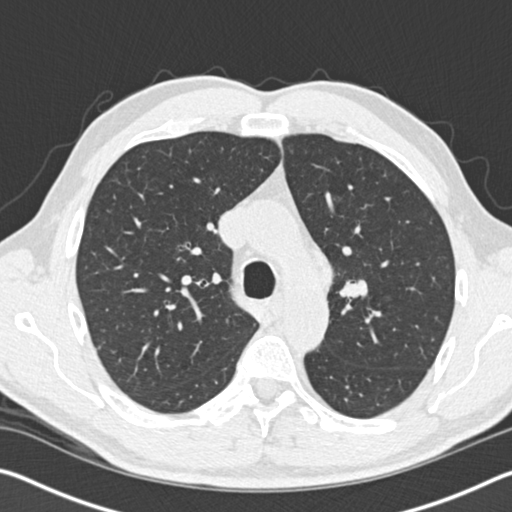
Low-dose screening chest CT, axial slice, baseline screening round, lung window (W 1500 / L -600 HU), 2 mm slice thickness, standard (soft-tissue) reconstruction kernel (B30f), 512 × 512 image matrix. Male, age 61 years at enrolment. Former smoker at enrolment.
Lesion marked by an expert reader, bounding box (x1, y1, x2, y2) in pixels: (343, 274, 373, 314). The screening reader recorded 2 non-calcified nodules or masses ≥4 mm on this exam; which of them this box marks is not recorded. Official screen result: positive, change unspecified: nodule(s) >= 4 mm or enlarging nodule(s), mass(es), or other non-specific abnormalities suspicious for lung cancer. Lung cancer was diagnosed 183 days after this screen: small cell carcinoma, NOS, left upper lobe, stage IIIB (AJCC 6th edition), 100 mm at pathology.